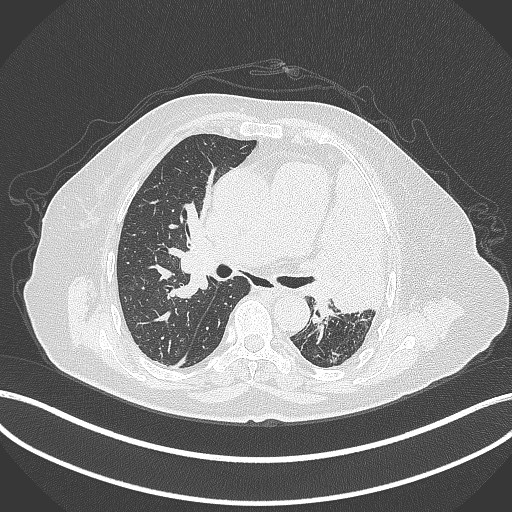
Chest CT, one axial slice; position 228 of 399 along the scan axis; reconstruction kernel B70f; 120 kVp; lung window (W 1500 / L -600 HU); 1 mm slice thickness; 512 × 512 image matrix. Female patient, age 75 years. From the clinical record (not read from this slice): clinical TNM (as recorded): T3 N3 M1.
Outlined on this slice (bounding box drawn by a radiologist):
- lung tumour (recorded histology: adenocarcinoma): bounding box [x1, y1, x2, y2] px = [303, 156, 388, 319]